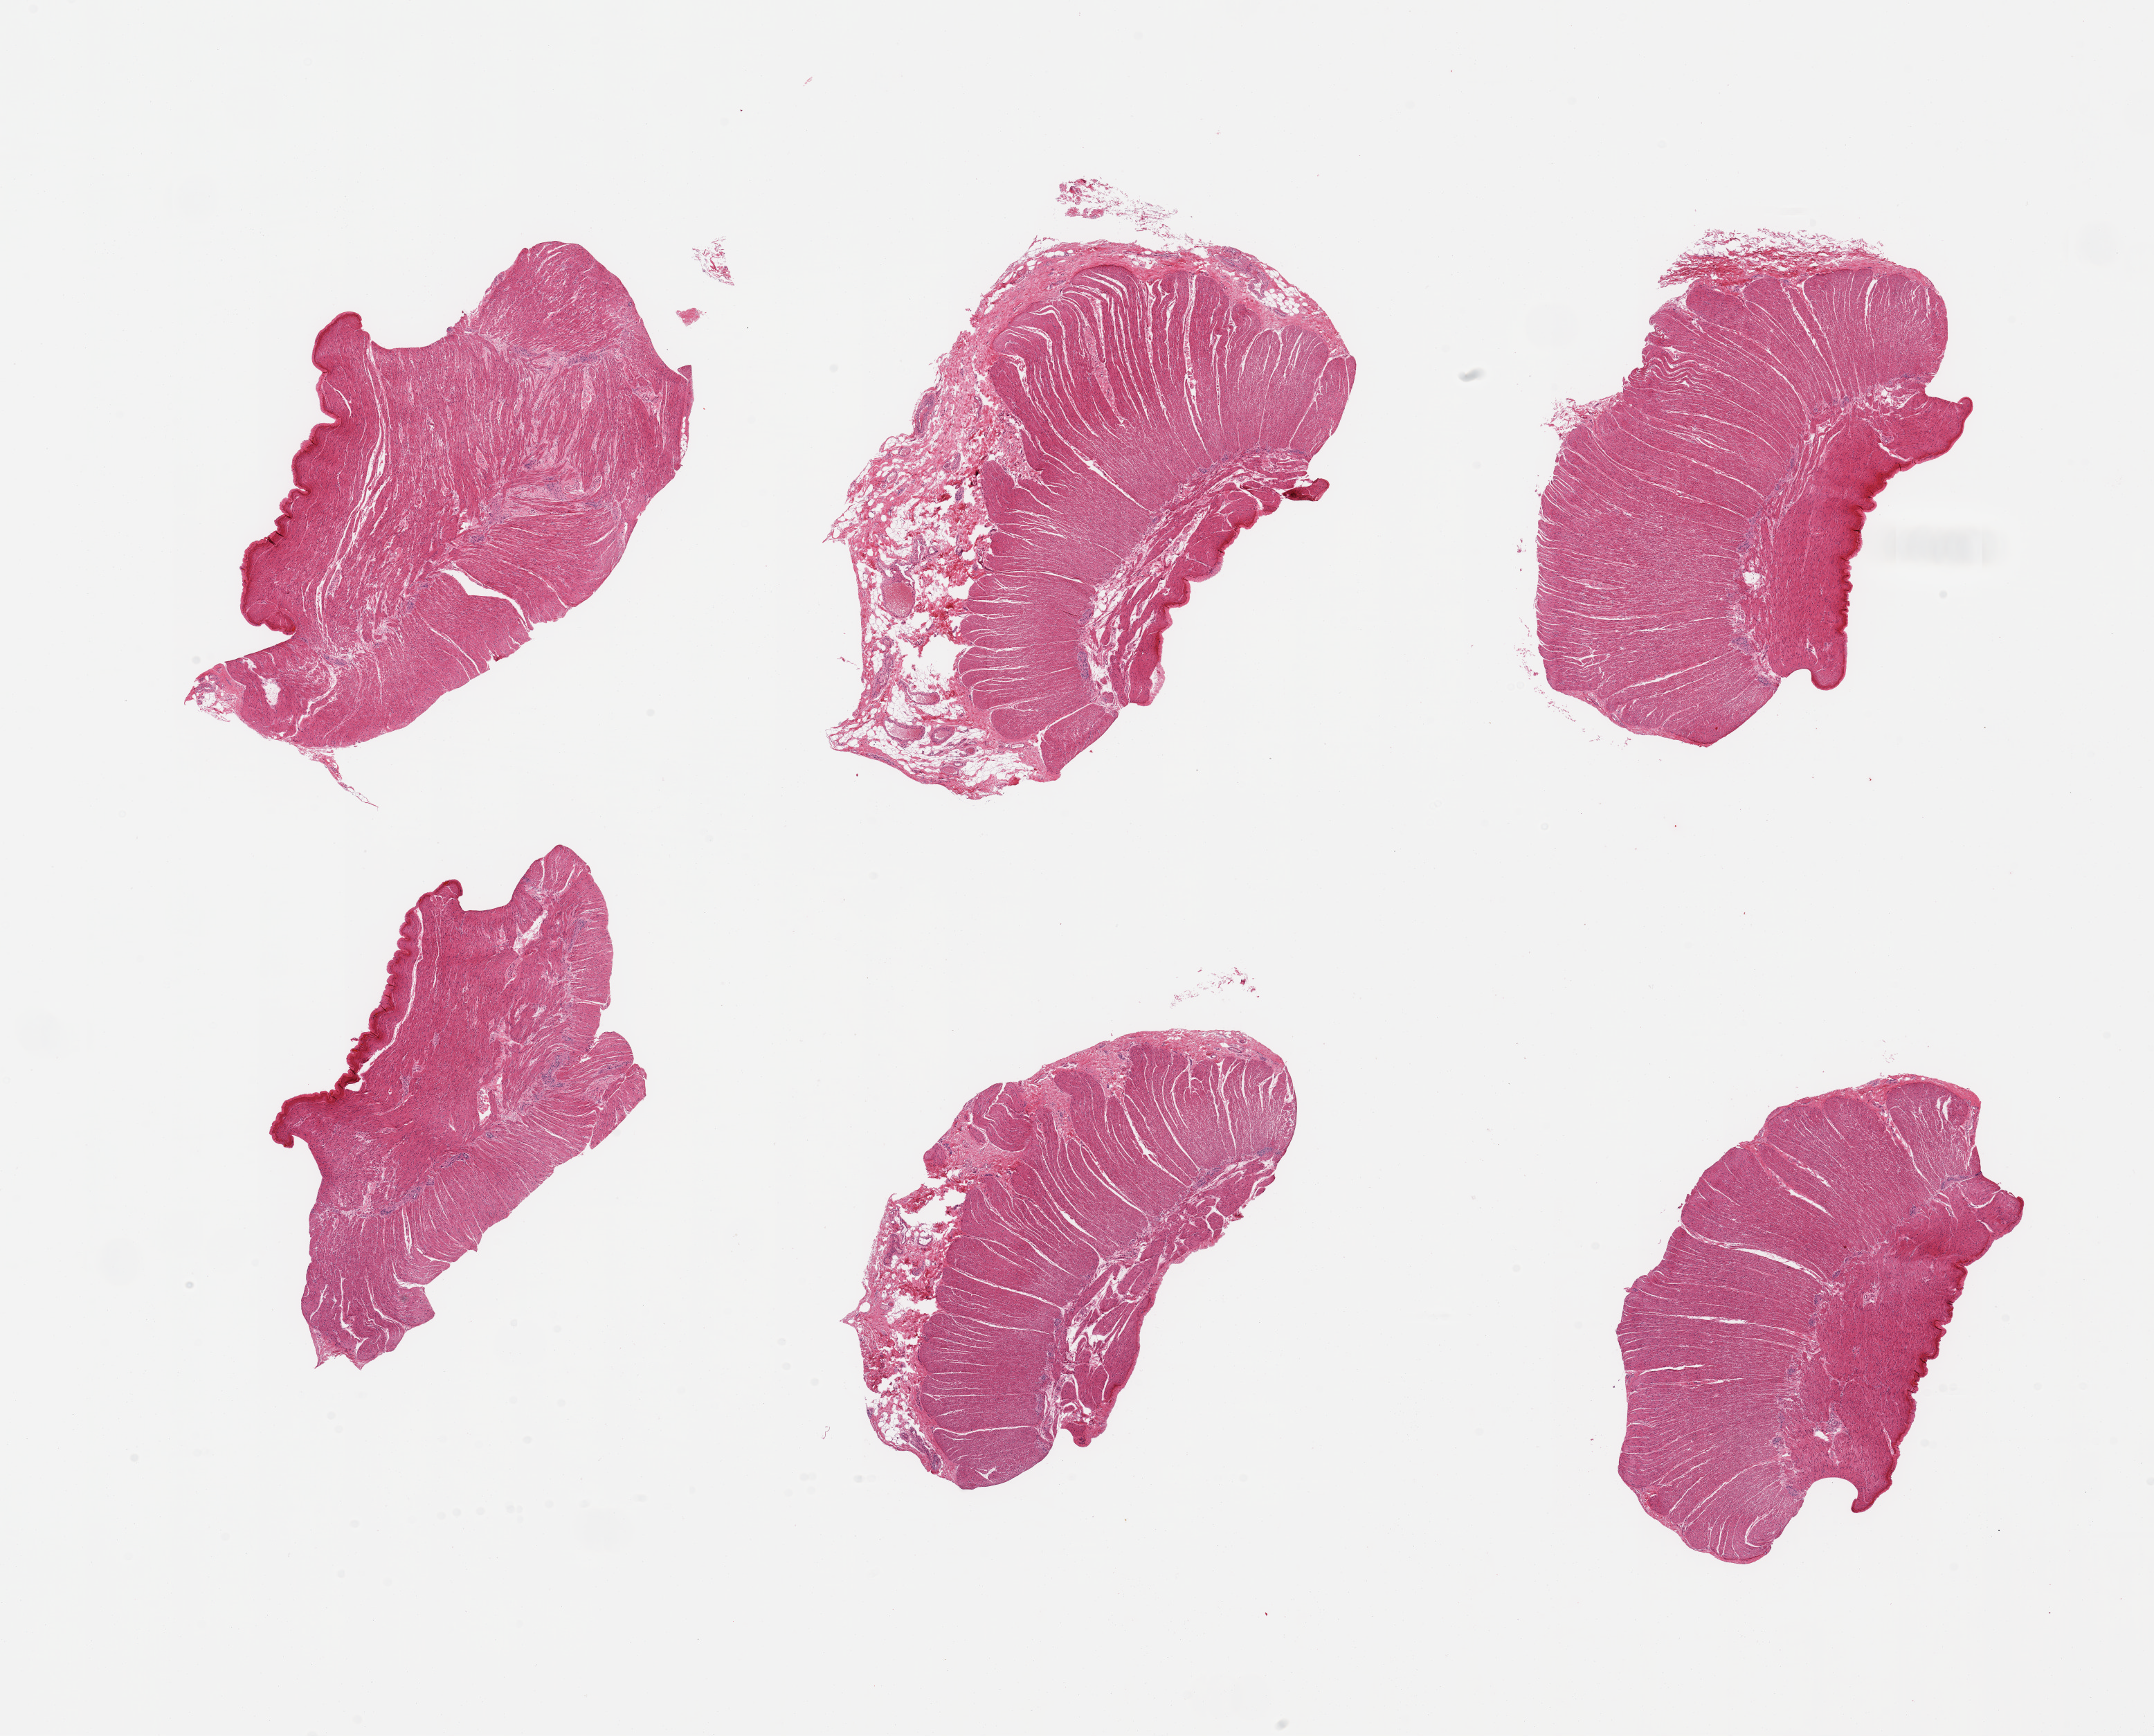
Digitized hematoxylin and eosin (H&E)-stained section, a low-resolution overview of the entire scanned area, about 24.6 x 19.8 mm. PAXgene-fixed, paraffin-embedded tissue. Sampled site (target tissue): sigmoid colon. Donor tissue sample. Donor: male.
• reviewer comment on this tissue sample: 6 pieces, confirmed target muscularis